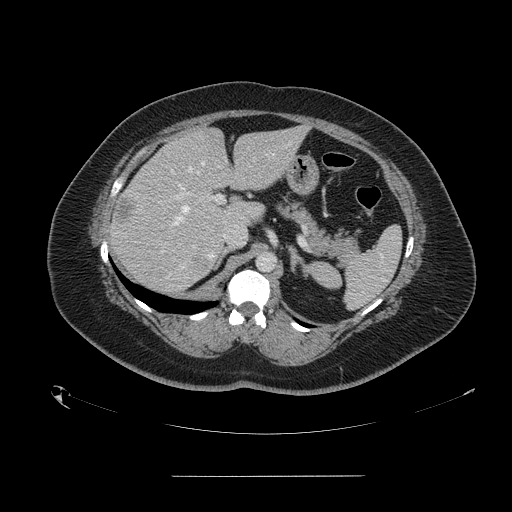
Contrast-enhanced abdominal CT, one axial slice; slice 97 of 164 in the series (ordered by position); soft-tissue window (W 400 / L 40 HU); 512 × 512 image matrix, field of view 495 × 495 mm. Female patient, age 52 years. From the clinical record (not read from this slice): diagnosis: colorectal cancer liver metastases, imaged before liver resection; multiple liver metastases: yes; largest metastasis: 3.5 cm; disease in both lobes: no.
Annotated regions visible in this slice (manually delineated by an expert):
- hepatic veins: bounding box [x1, y1, x2, y2] px = [171, 161, 204, 226]
- liver: [111, 128, 305, 293]
- planned liver remnant (the part of the liver to remain after resection): [175, 128, 305, 228]
- portal vein (with intrahepatic branches): [169, 170, 225, 204]
- liver metastasis: [192, 255, 210, 271]
- liver metastasis: [115, 200, 134, 227]